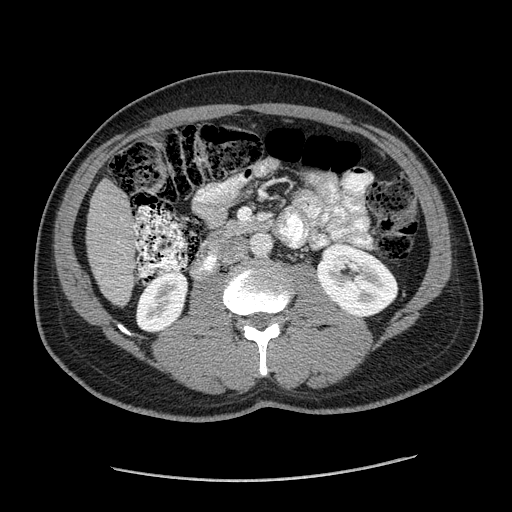
Contrast-enhanced abdominal CT (liver protocol), one axial slice; position 45 of 182 along the scan axis; reconstruction kernel STANDARD; soft-tissue window (W 400 / L 40 HU); 512 × 512 image matrix, field of view 400 × 400 mm. From the clinical record (not read from this slice): diagnosis: hepatocellular carcinoma (patient treated with transarterial chemoembolisation; whether this scan precedes or follows treatment is not stated here); TNM stage (as recorded): Stage-I.
Outlined on this slice (semi-automatically segmented with operator editing):
- liver parenchyma outside the tumour (the mass and vessels are separate outlines, so this box may not span the whole liver): bounding box (x1, y1, x2, y2) in pixels: (86, 178, 138, 304)
- liver vessels: (136, 231, 138, 233)